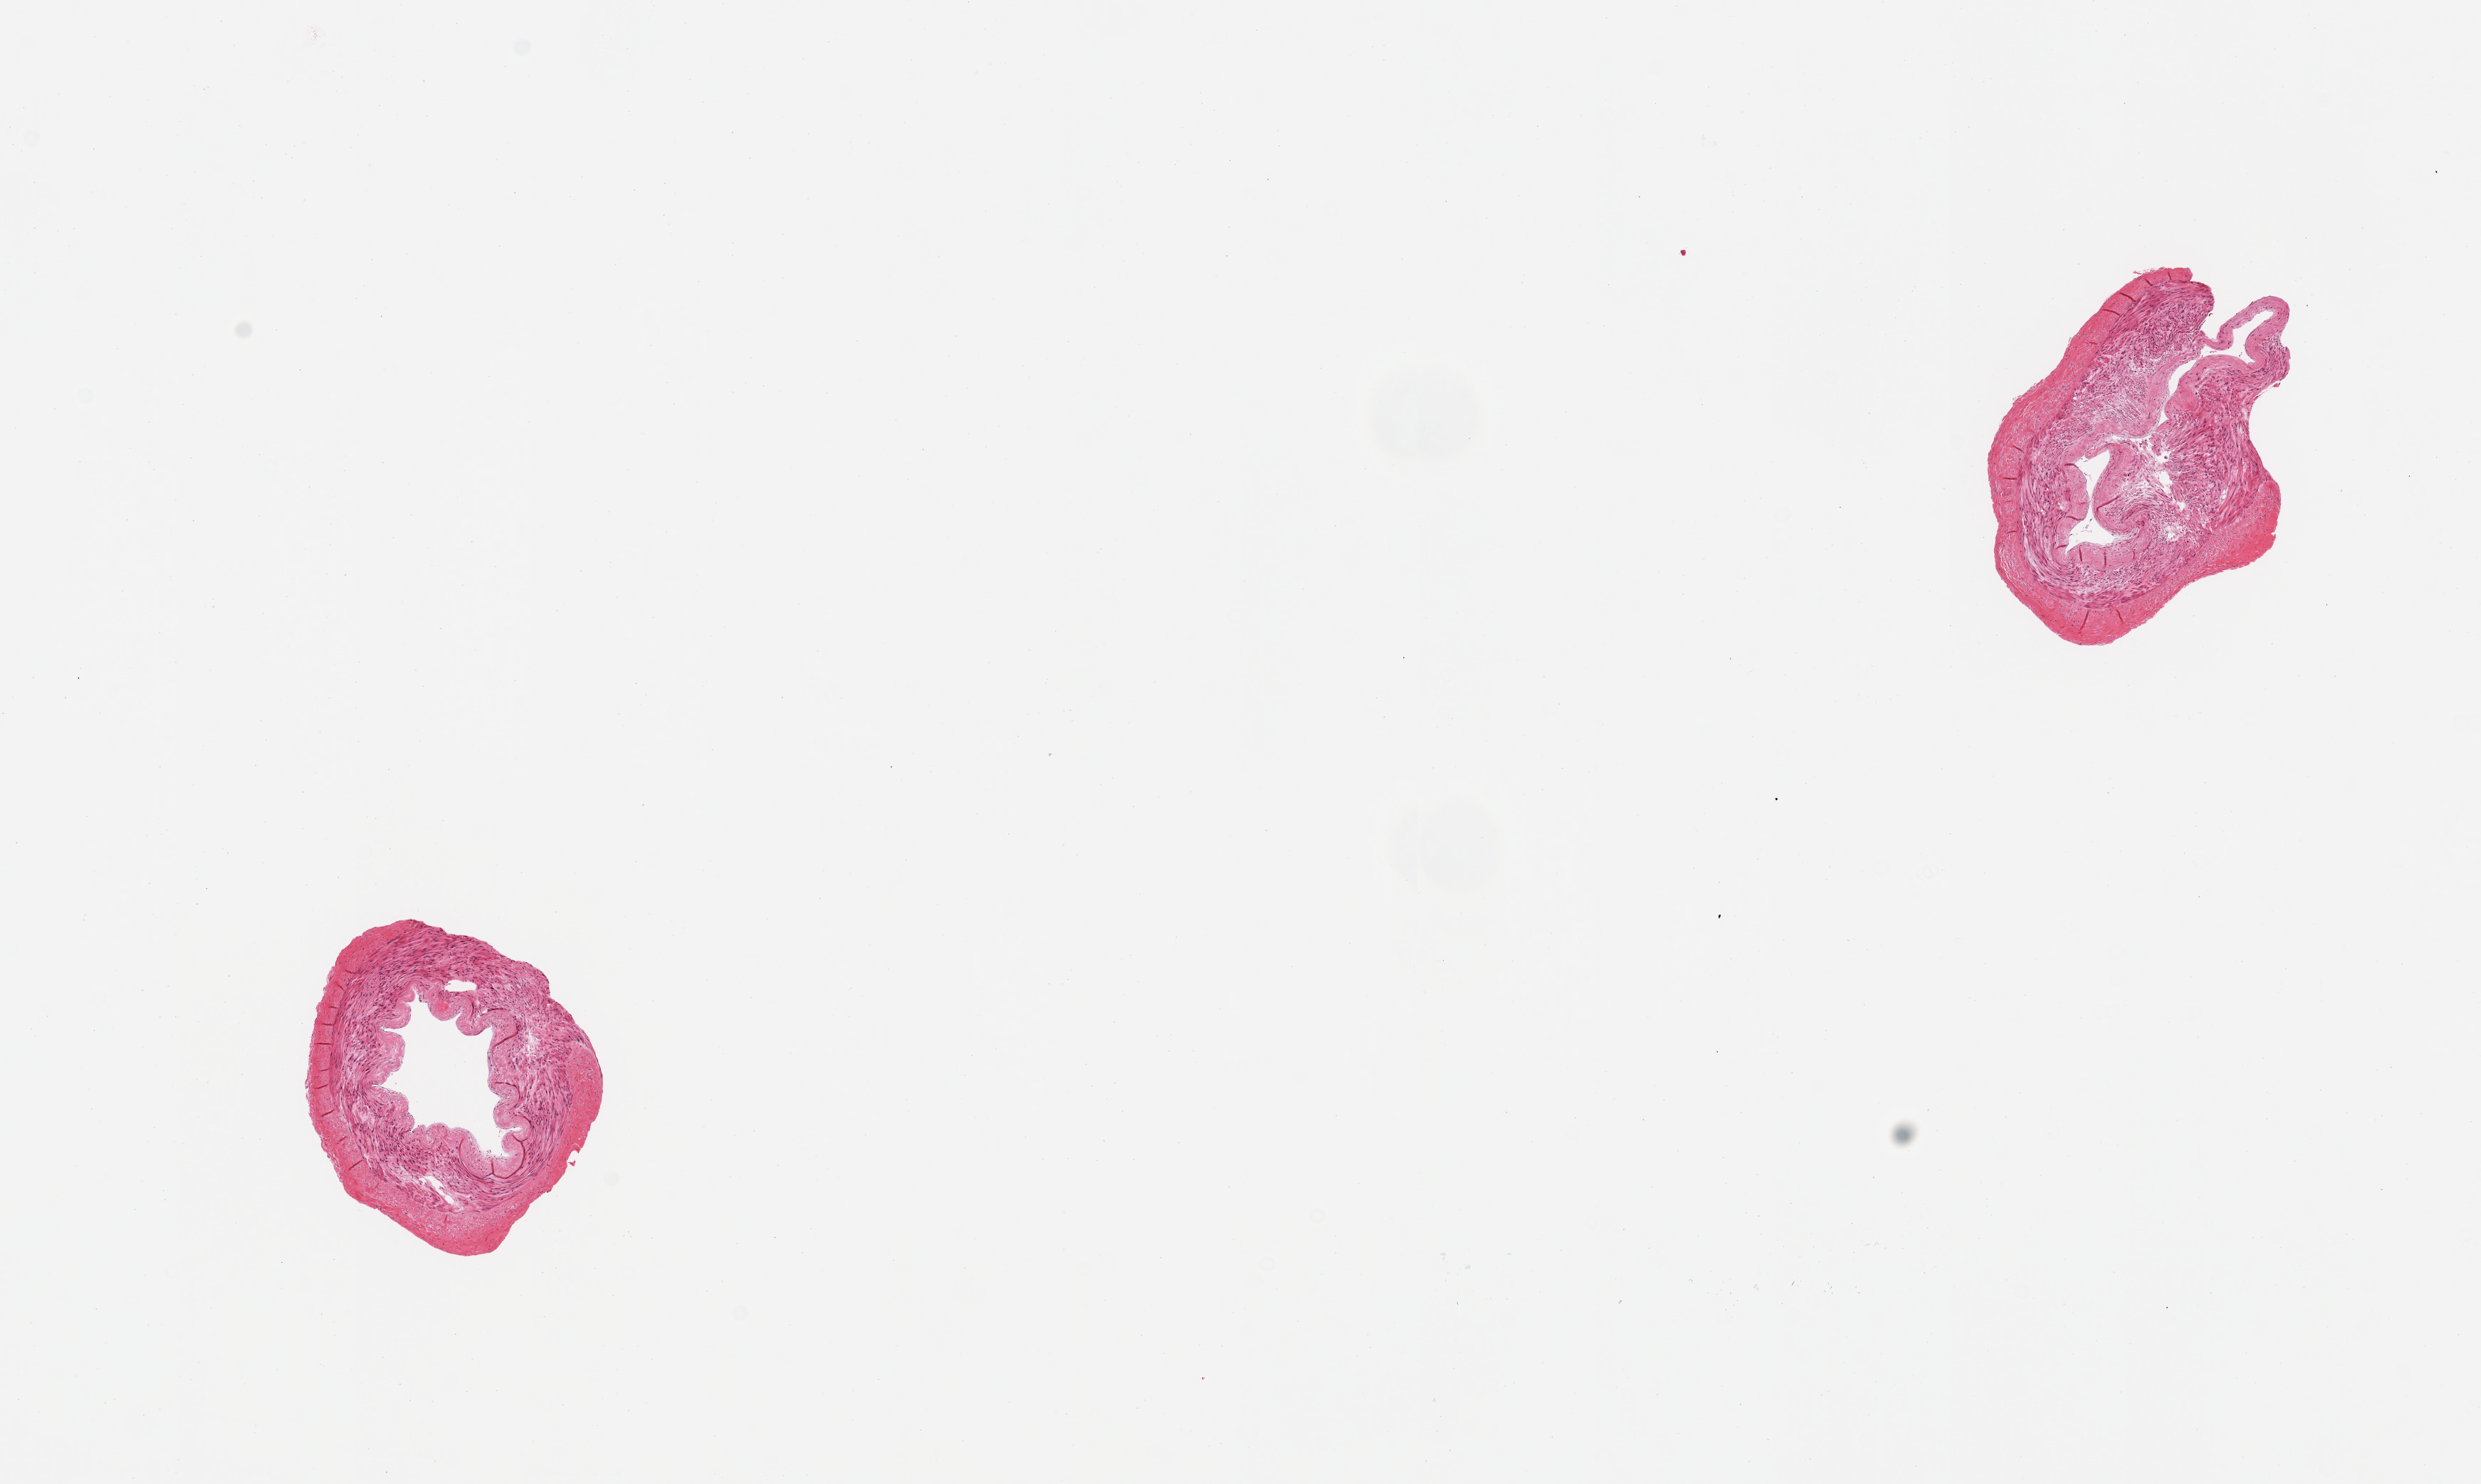
H&E whole-slide image, shown as a low-resolution overview of the whole scanned area (about 13.8 x 8.2 mm, slide scanned at 20x); PAXgene-fixed, paraffin-embedded tissue; section of tibial artery (target tissue); tissue donor sample.
Review note (as recorded): 2 pieces, no significant adherenat fat, or atherosis.